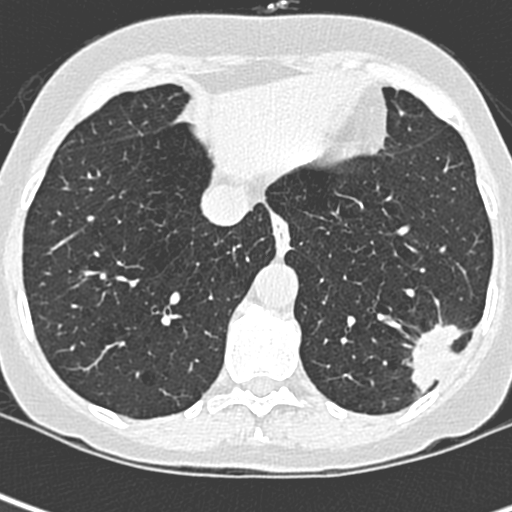
Low-dose screening chest CT, one axial slice; slice 80 of 252 in the series (ordered by position); 120 kVp; lung window (W 1500 / L -600 HU); 1.3 mm slice thickness; 512 × 512 image matrix, field of view 271 × 271 mm.
Outlined on this slice (expert manual segmentation):
- lesion 1 (tumor, lower lobe of left lung): bounding box <411,321,465,397> (left, top, right, bottom; pixels)